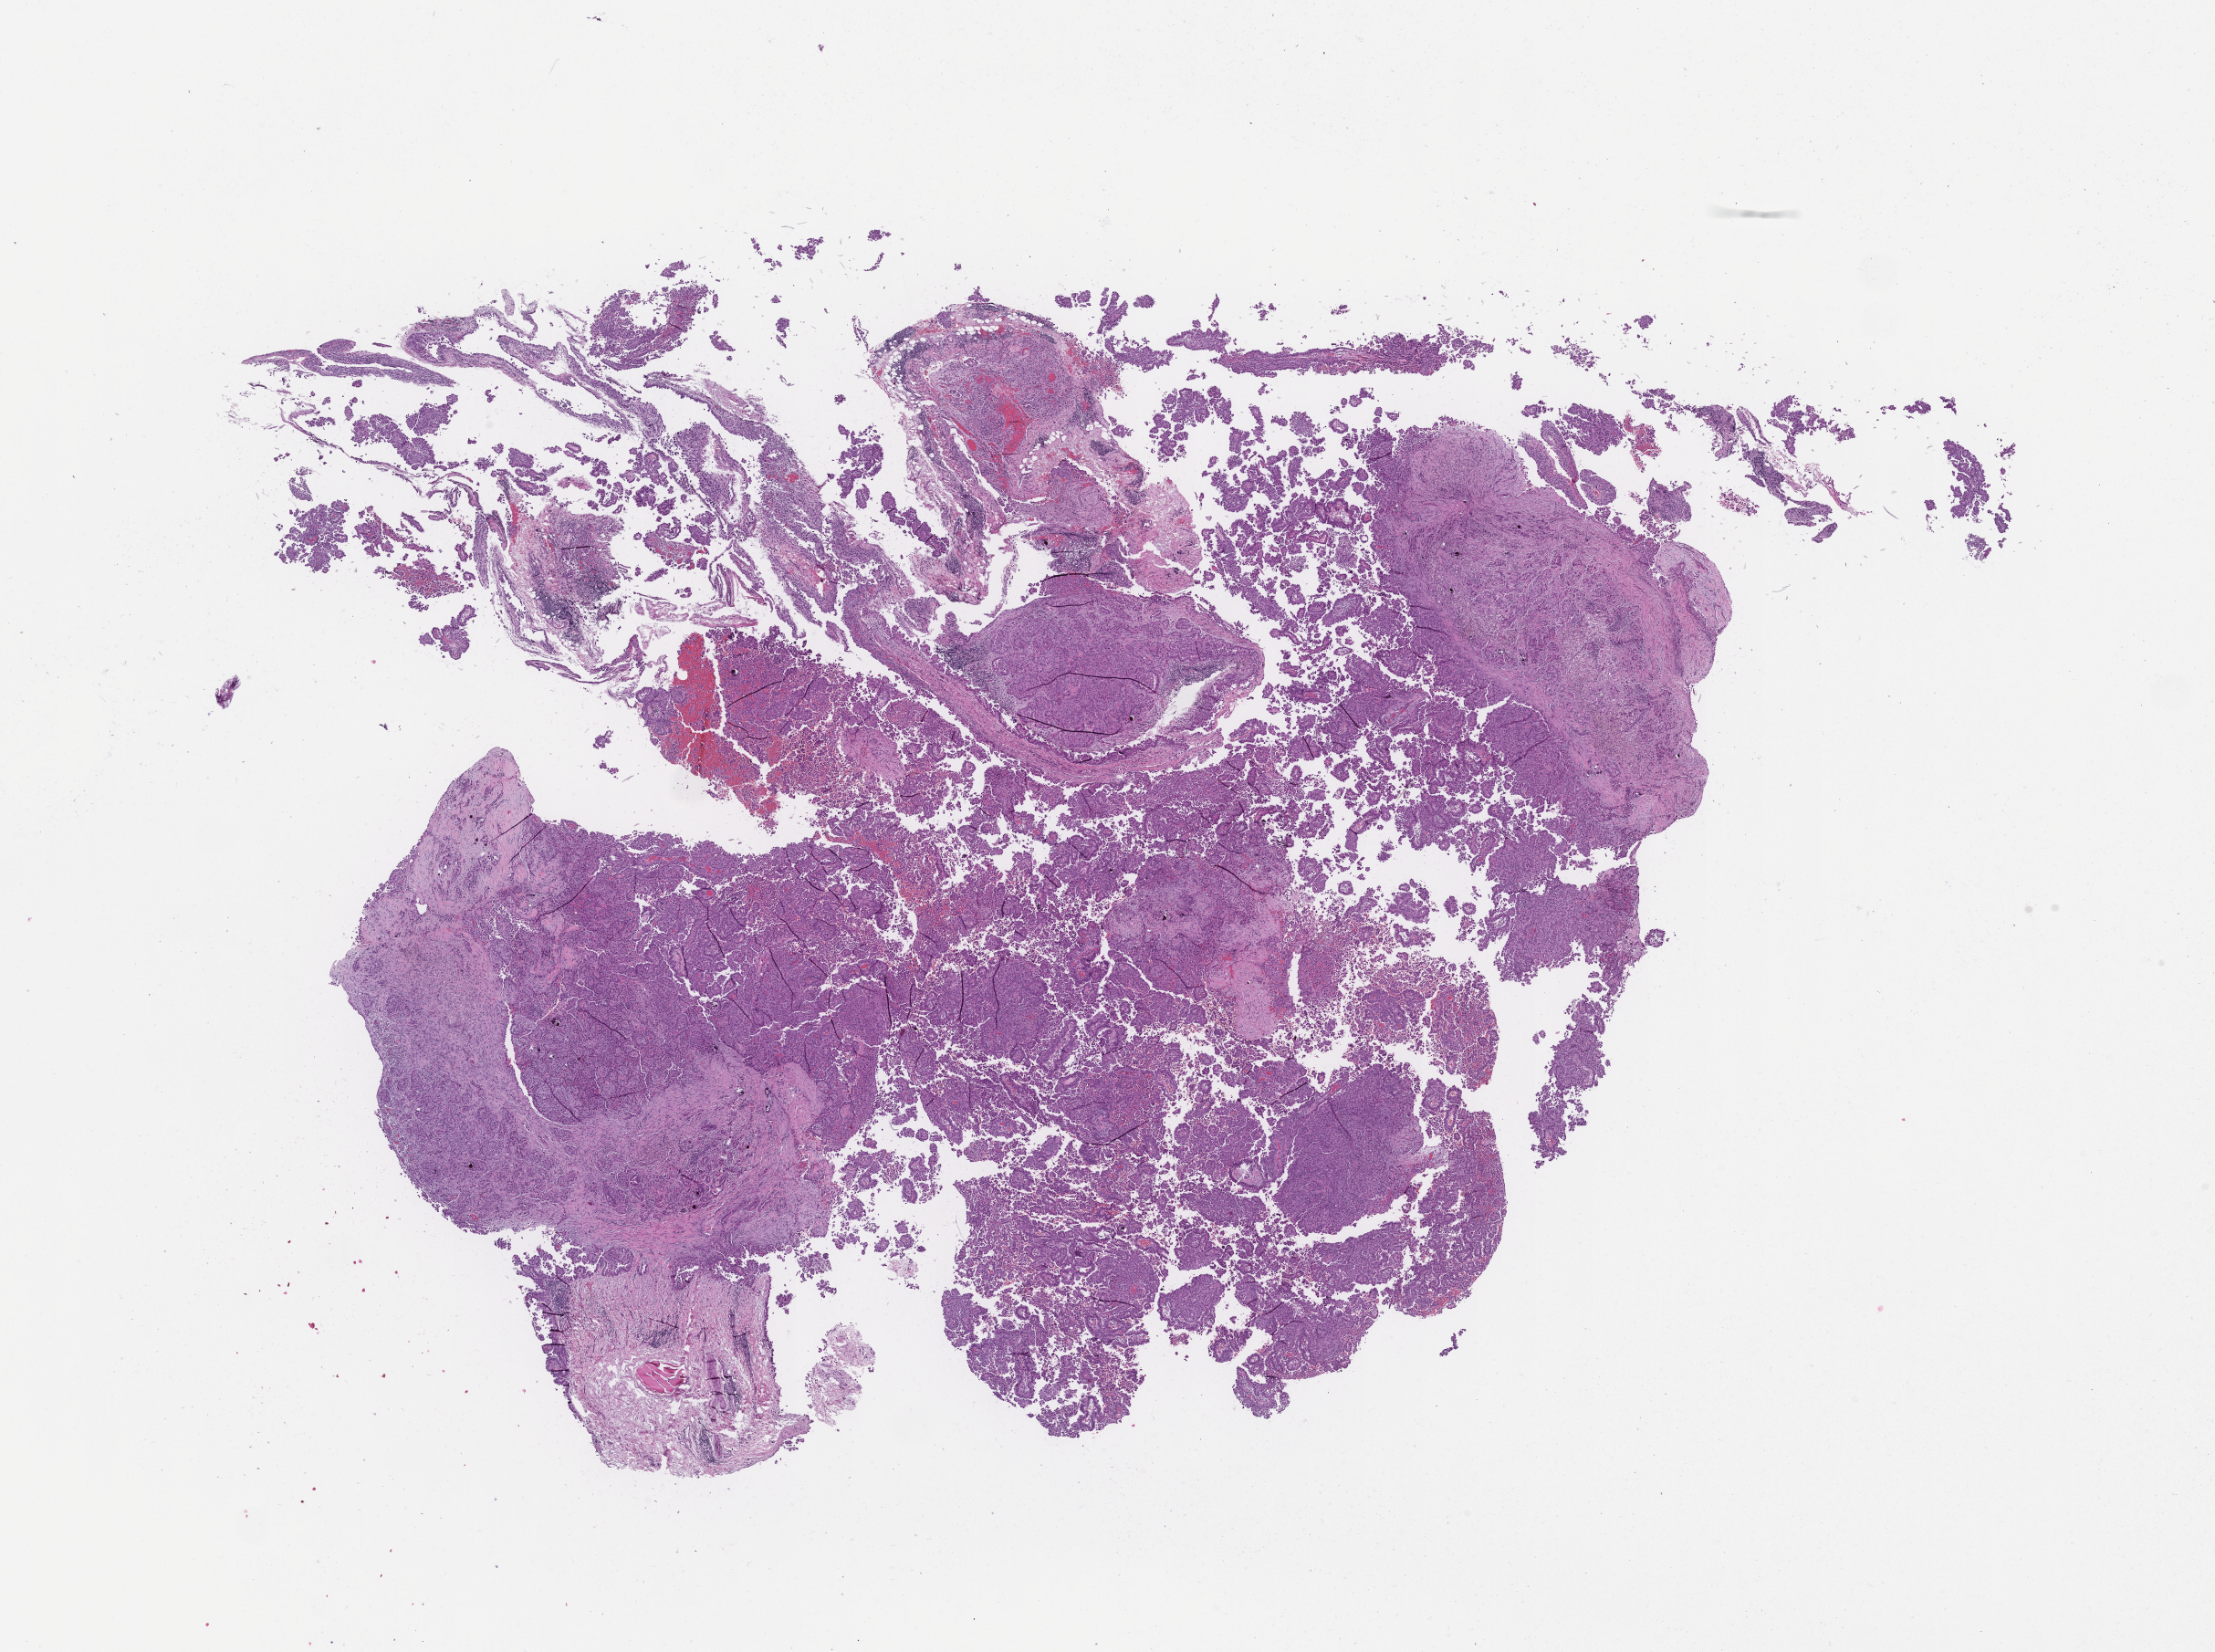
Digitized haematoxylin and eosin-stained section, a low-resolution overview of the entire scanned area, about 19.6 x 14.6 mm; FFPE section; specimen time point: archival tissue. Patient: female.
This section: metastasis (sampled organ not recorded). Patient diagnosis (primary): Non-Small Cell Lung Carcinoma.